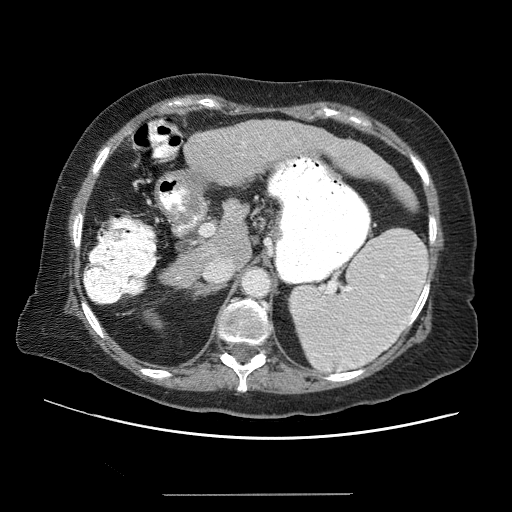
Contrast-enhanced abdominal CT (liver protocol), one axial slice. Slice 34 of 65 in the series (ordered by position). Reconstruction kernel STANDARD. Soft-tissue window (W 400 / L 40 HU). 2.5 mm slice thickness. 512 × 512 image matrix, field of view 380 × 380 mm. From the clinical record (not read from this slice): diagnosis: hepatocellular carcinoma (patient treated with transarterial chemoembolisation; whether this scan precedes or follows treatment is not stated here); TNM stage (as recorded): Stage-IIIB; Child-Pugh class: A; tumour nodularity: uninodular.
Outlined on this slice (semi-automatically segmented with operator editing):
- liver parenchyma outside the tumour (the mass and vessels are separate outlines, so this box may not span the whole liver): bounding box <156,120,419,295> (left, top, right, bottom; pixels)
- liver vessels: <188,130,375,263>